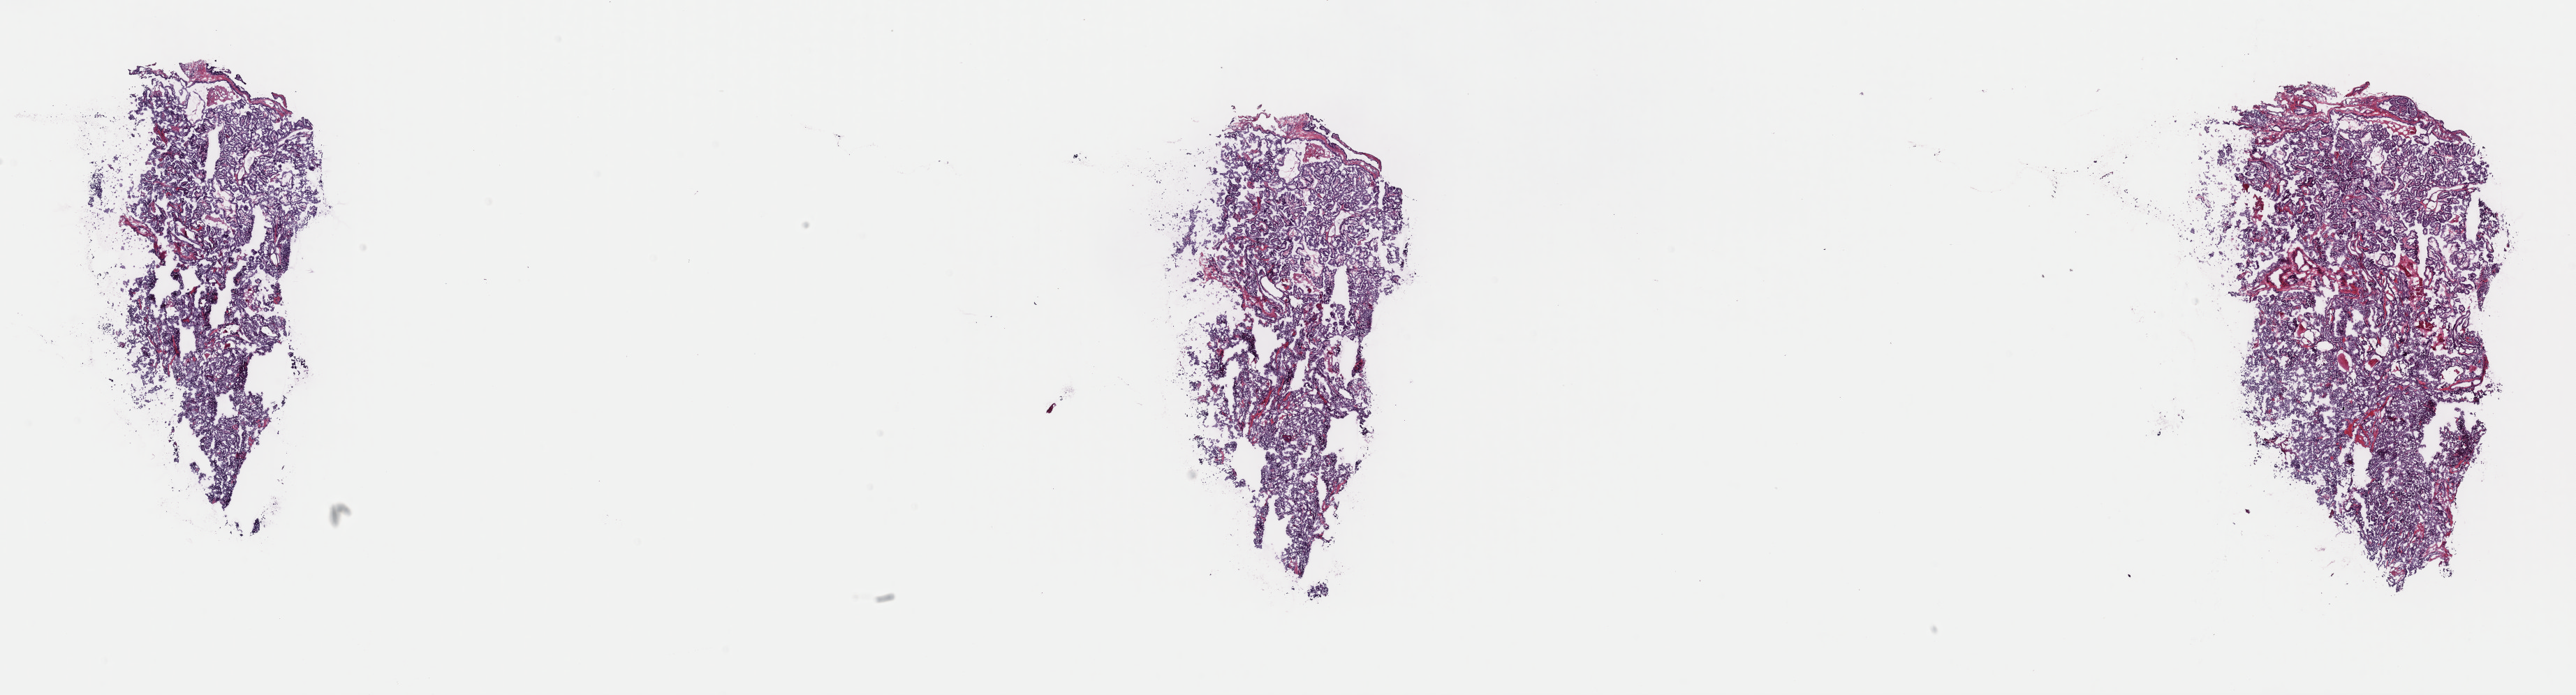
Whole-slide histology image, Hematoxylin and eosin (H&E) stained, shown as a low-resolution overview of the whole scanned area (about 29.1 x 7.9 mm, acquisition: 40x scan), frozen section, primary tumour sample from the thyroid. Patient: female, age at initial diagnosis 39 years.
Pathologic diagnosis: Papillary adenocarcinoma, NOS (thyroid gland).